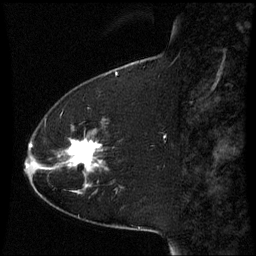
Breast MRI (dynamic contrast-enhanced), one sagittal slice; slice 14 of 60 in the series (ordered by position); dynamic contrast-enhanced series, image 2 of 3 at this slice position (ordered by acquisition); 1.5 T; TE 4.2 ms, TR 8.9 ms; 2.3 mm slice thickness; 256 × 256 image matrix. Female patient, age 51 years. Case-level facts recorded for this patient, not image findings: setting: breast cancer imaged before/during neoadjuvant chemotherapy; receptor status: HR-positive, HER2-negative.
Outlined on this slice (semi-automatic segmentation, software-assisted and operator-edited):
- analysis volume of interest (the breast-tissue region the enhancement analysis was run in; not a lesion): bounding box <50,124,109,187> (left, top, right, bottom; pixels)
- tumour enhancement mask (voxels above the 70 % enhancement threshold inside the analysis volume of interest): <70,141,101,167>